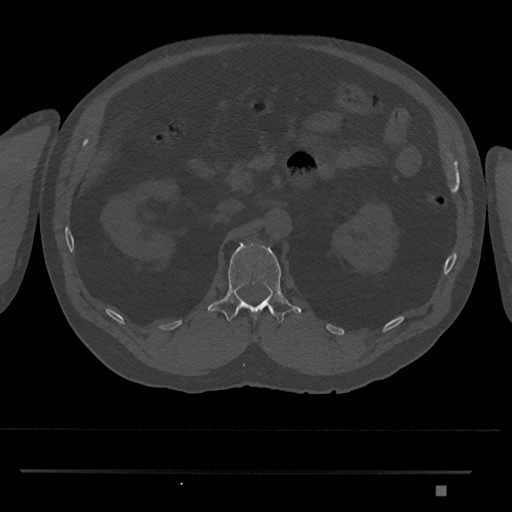
CT including the spine, one axial slice. Slice 827 of 1134 in the series (ordered by position). Bone window (W 1800 / L 400 HU). 512 × 512 image matrix, field of view 429 × 429 mm. Patient: male, 65 years. Case-level facts recorded for this patient, not image findings: primary cancer: prostate.
Outlined on this slice (semi-automatic segmentation, software-assisted and operator-edited):
- L1 vertebra: bounding box (x1, y1, x2, y2) in pixels: (208, 242, 301, 323)